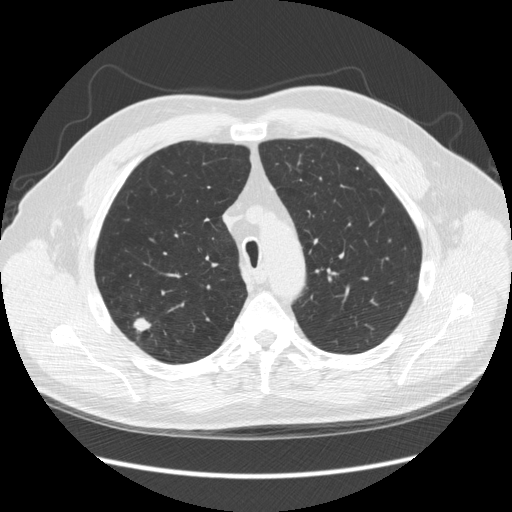
Chest CT (low-dose screening protocol), one axial image; third annual screen; lung window (W 1500 / L -600 HU); 120 kVp; slice 60 of 248 in the series. Male participant, aged 64 years at enrolment. Former smoker at enrolment.
Lesion marked by an expert reader, box from (x=118, y=313) to (x=169, y=355) px. The screening reader recorded 4 non-calcified nodules or masses ≥4 mm on this exam (right upper lobe, right upper lobe, right upper lobe, right upper lobe); which of them this box marks is not recorded. Lung cancer was diagnosed 15 days after this screen: adenocarcinoma, NOS, right upper lobe, moderately differentiated (G2), stage IA (AJCC 6th edition), 14 mm at pathology.